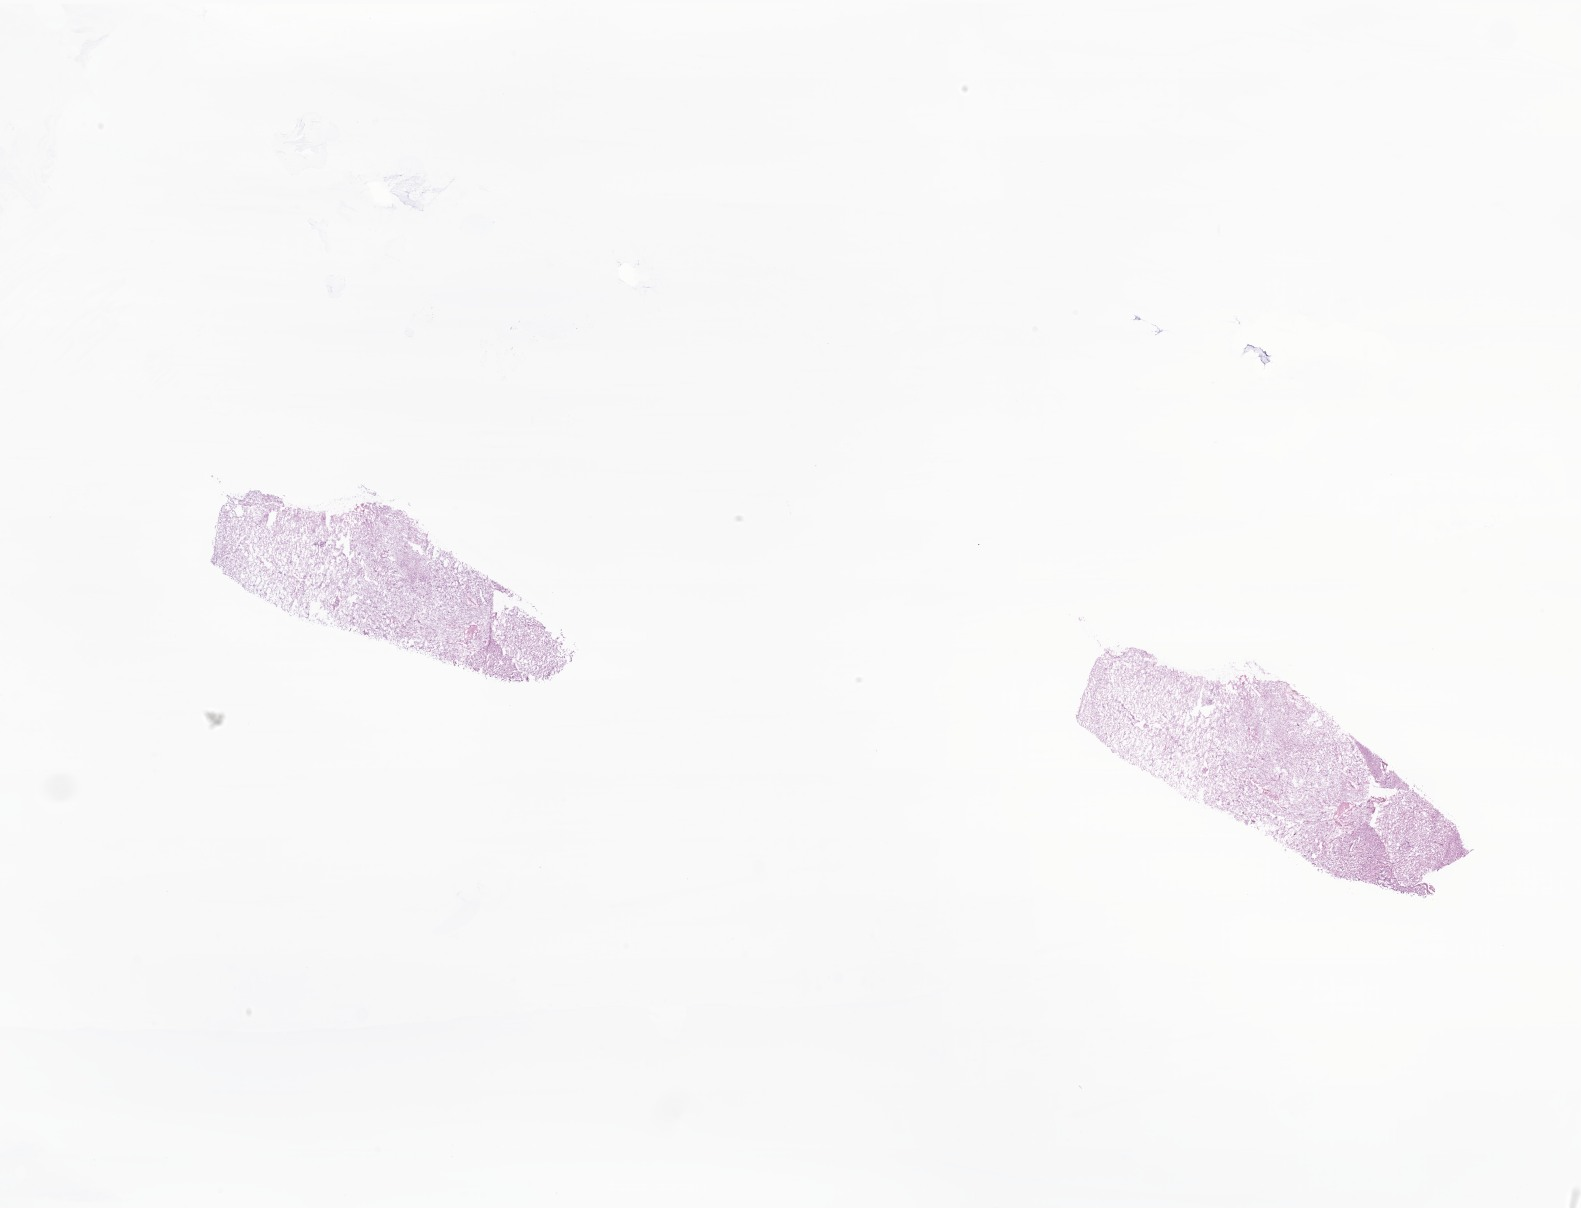
H&E whole-slide image of tumor tissue from the brain, low-resolution overview of the scanned area, about 26.7 x 20.4 mm, cryosection (OCT / tissue freezing medium). Male patient, age 193 months (16 years 1 month).
Recorded diagnosis: Neoplasm, uncertain whether benign or malignant.